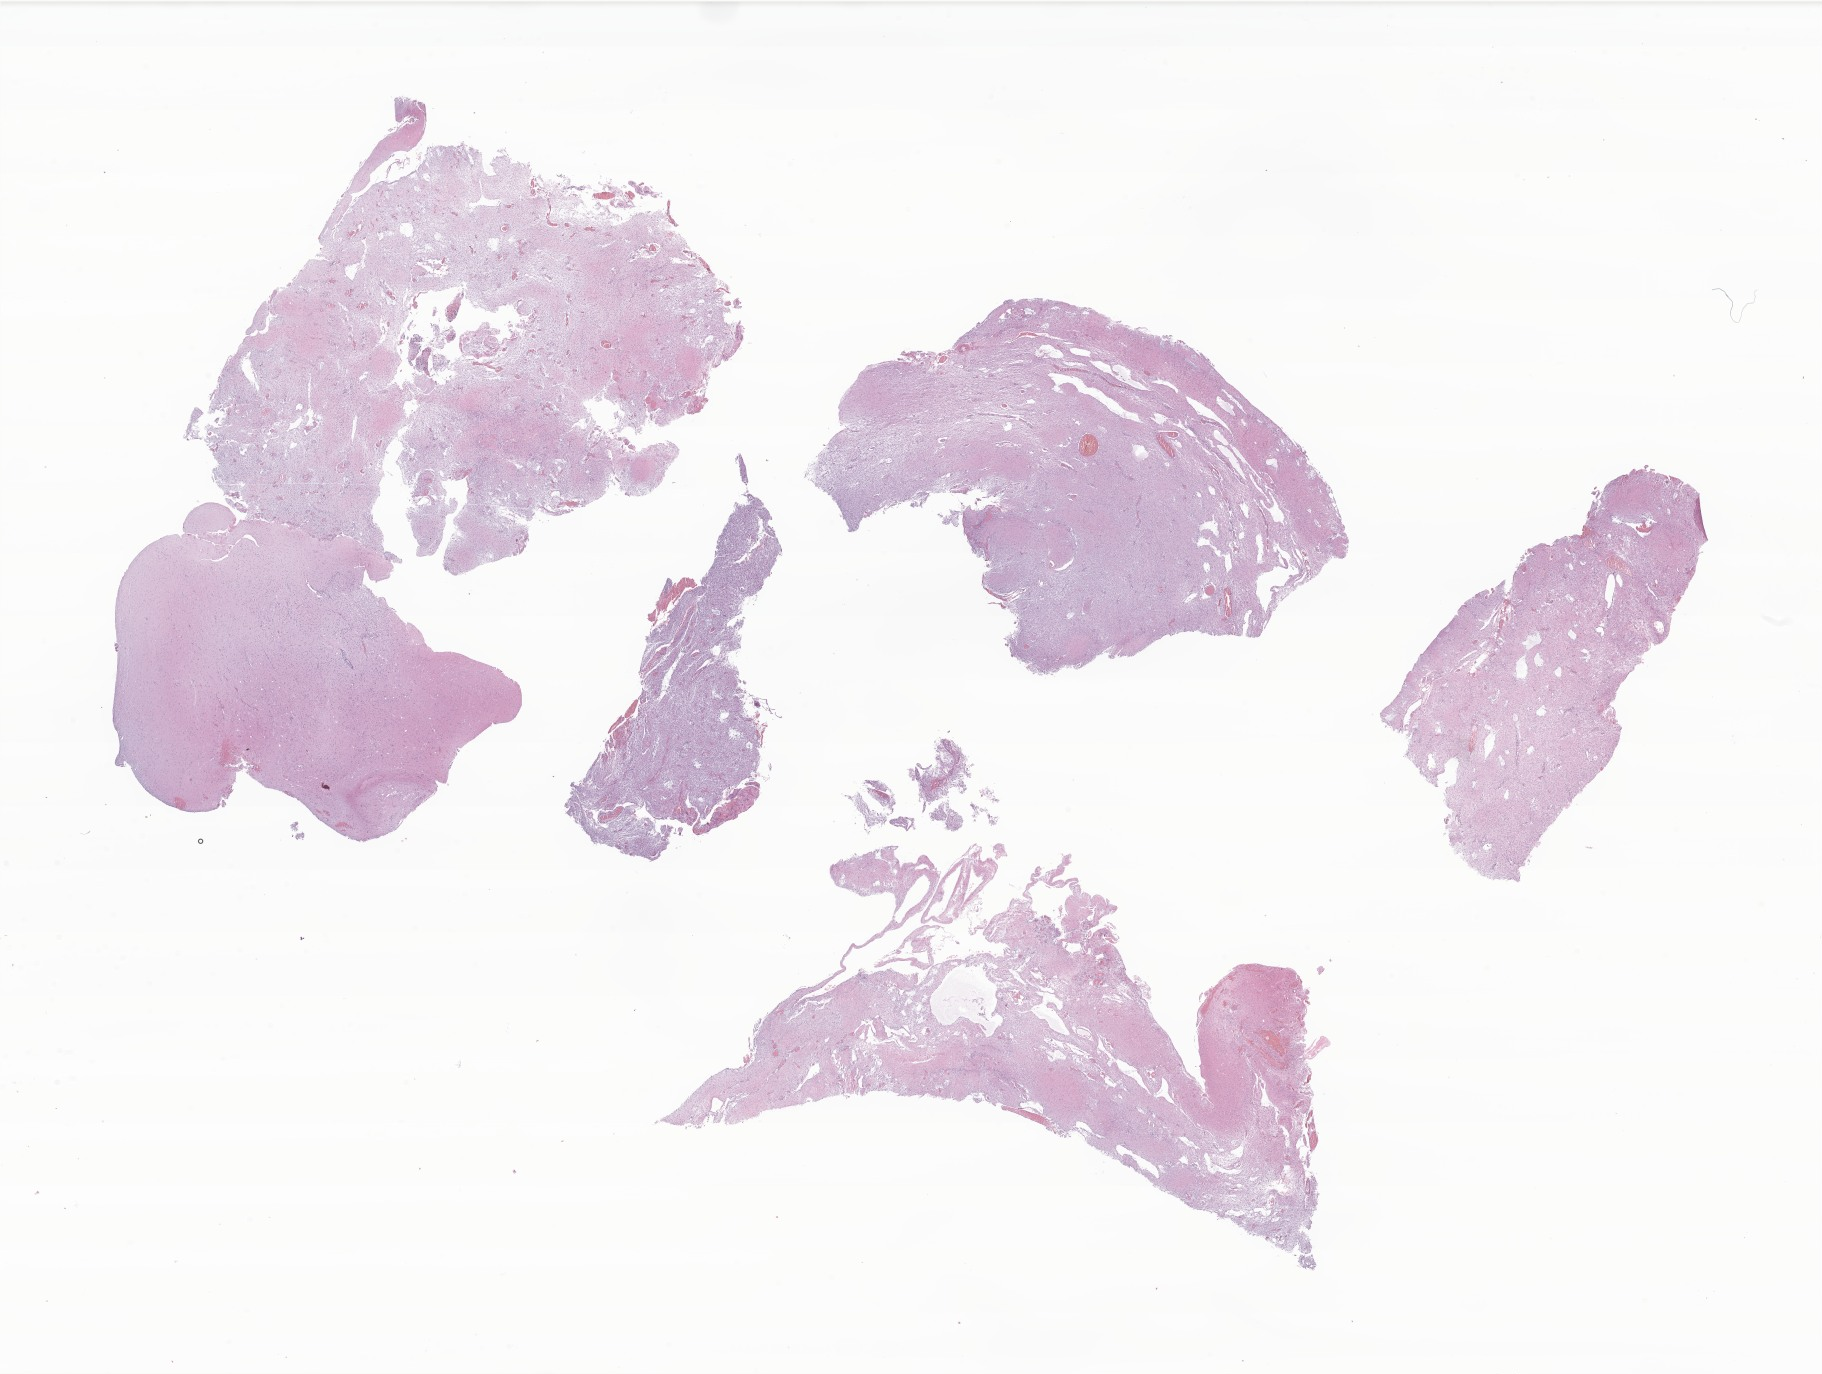
Whole-slide image, hematoxylin and eosin (H&E) stain of tumor tissue from the brain — low-resolution overview of the scanned area, about 30.7 x 23.2 mm, formalin-fixed paraffin-embedded section. Patient female; age 146 months (12 years 2 months).
Diagnosis: Astrocytoma, NOS.